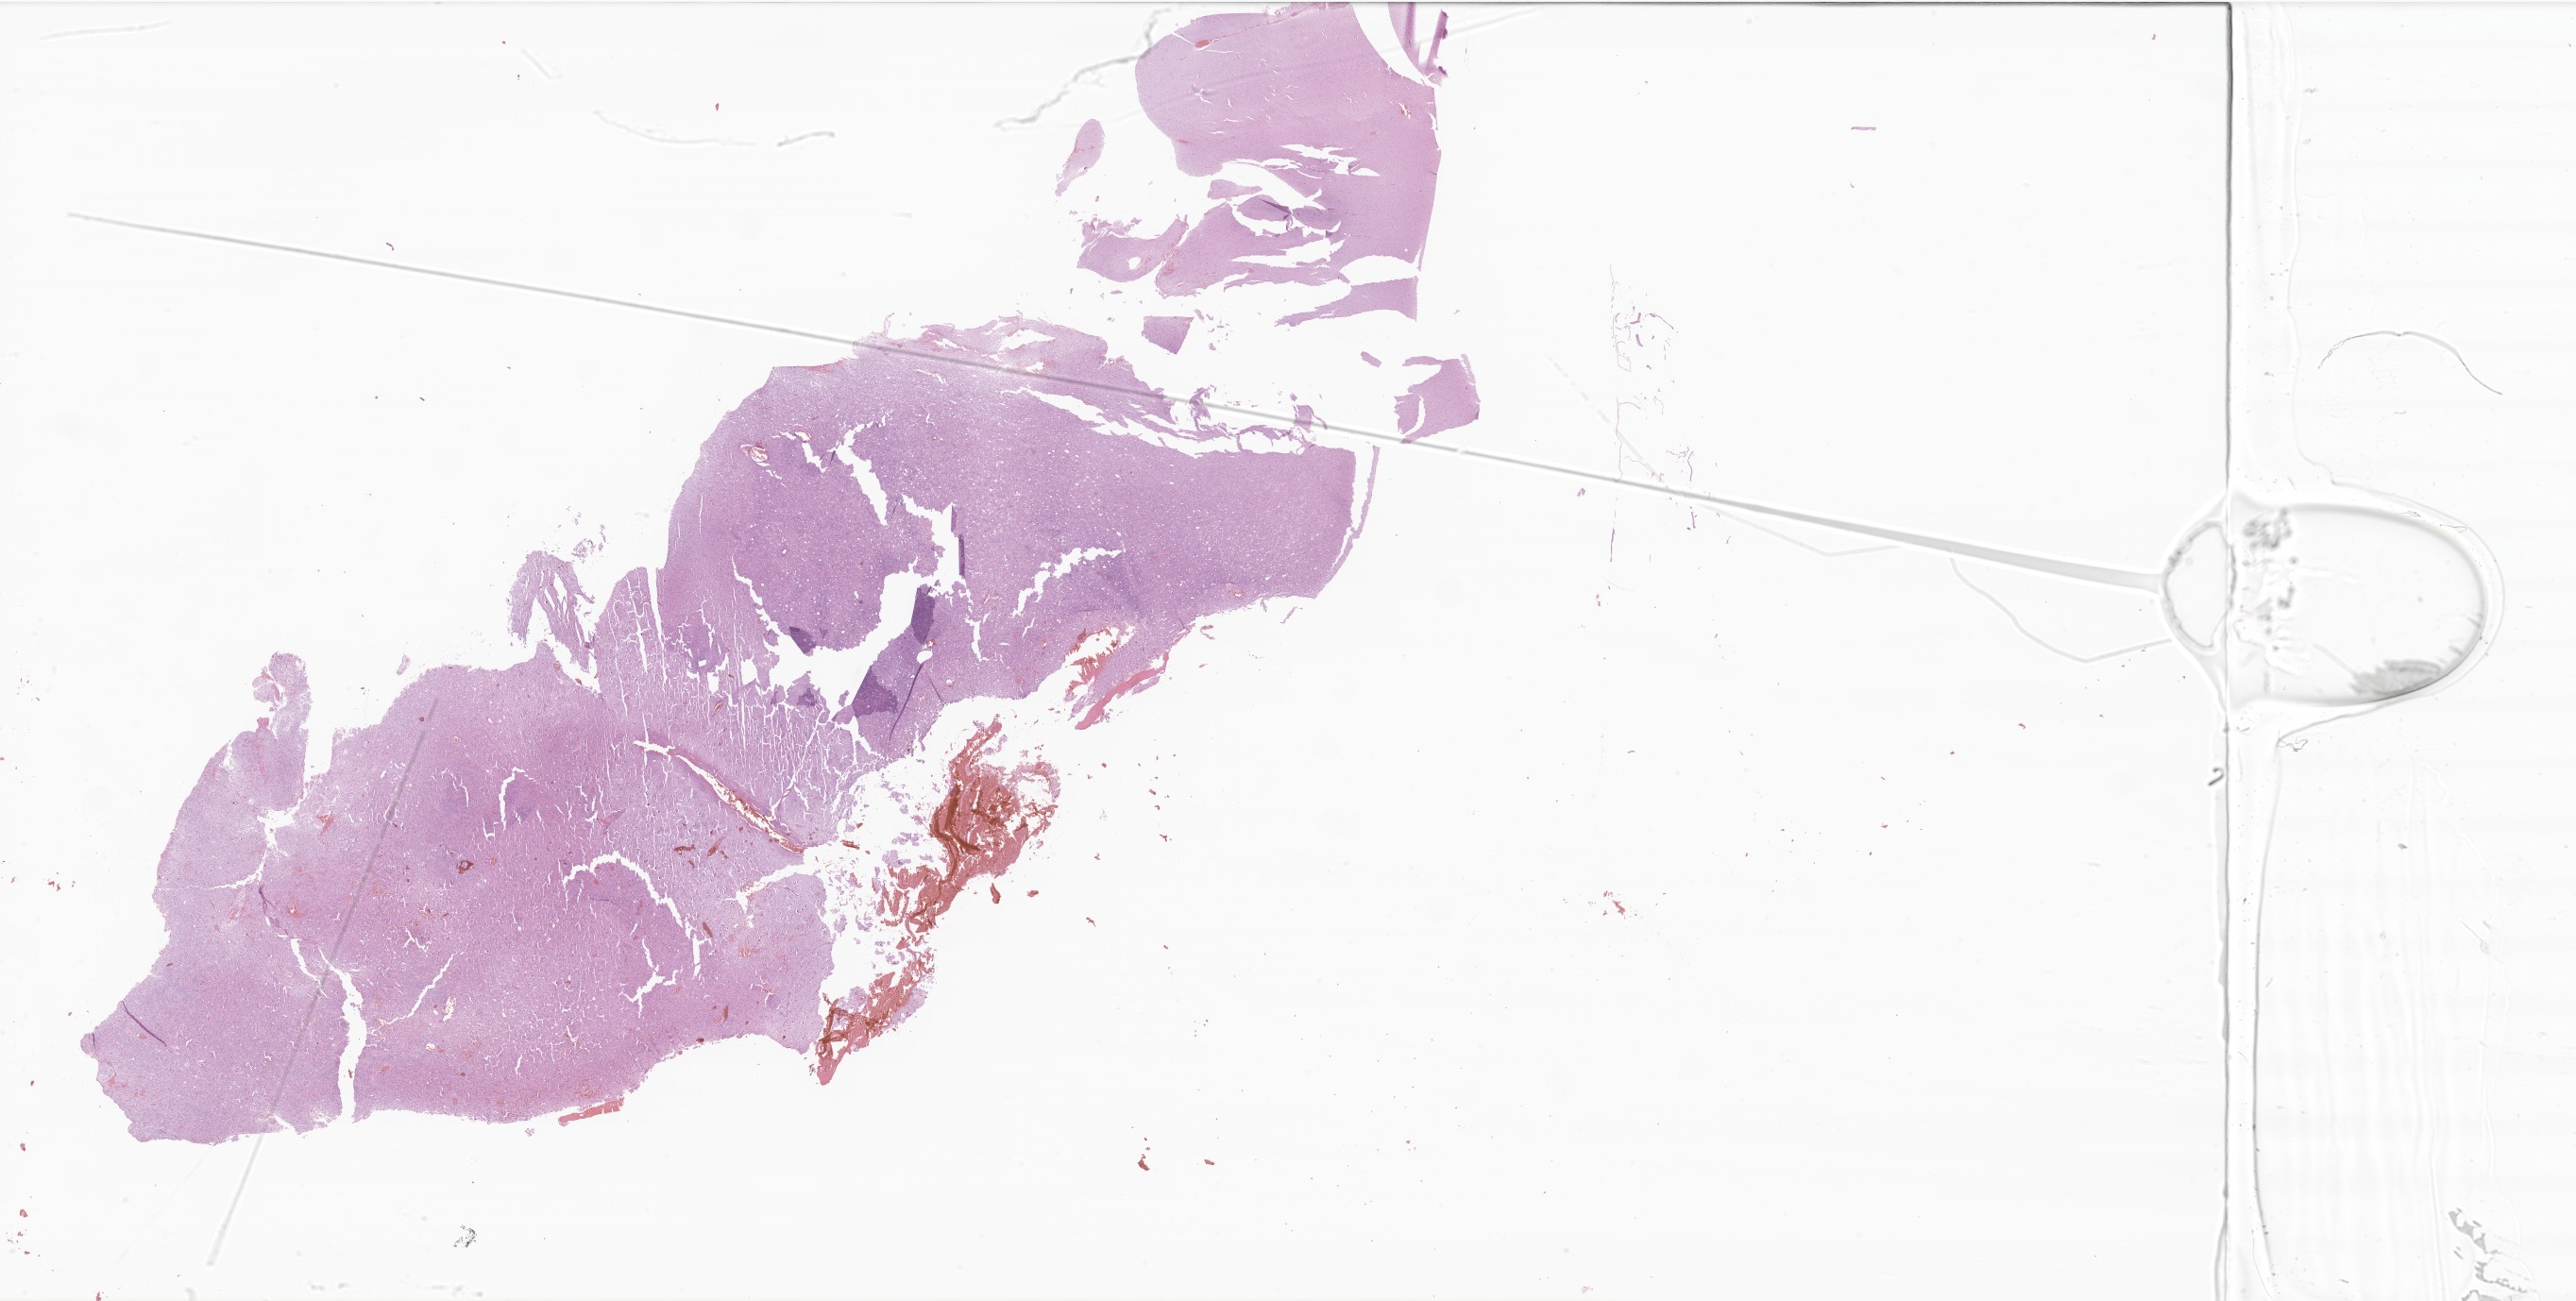
Digitized hematoxylin and eosin (H&E)-stained section of tumor tissue from the frontal lobe — low-resolution overview of the scanned area, about 46.0 x 23.2 mm, formalin-fixed, paraffin-embedded (FFPE) tissue. Female patient, age 262 months (21 years 10 months).
• recorded diagnosis: Astrocytoma, NOS